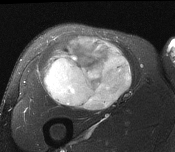
MRI of an extremity soft-tissue mass, one axial slice; position 96 of 116 along the scan axis; T2-weighted fat-saturated; MR volume resampled by the dataset authors to the PET/CT grid (not the native acquisition matrix); 3.27 mm slice thickness; 175 × 152 image matrix, field of view 171 × 148 mm. Male patient. From the clinical record (not read from this slice): histological type: pleiomorphic leiomyosarcoma; grade: intermediate; site of the primary tumour: right thigh.
Structures marked on this image (expert contour drawn on MRI and transferred to this co-registered scan by the dataset authors):
- gross tumour volume including surrounding oedema: bounding box [x1, y1, x2, y2] px = [44, 38, 134, 112]
- gross tumour volume (mass): [44, 38, 134, 112]